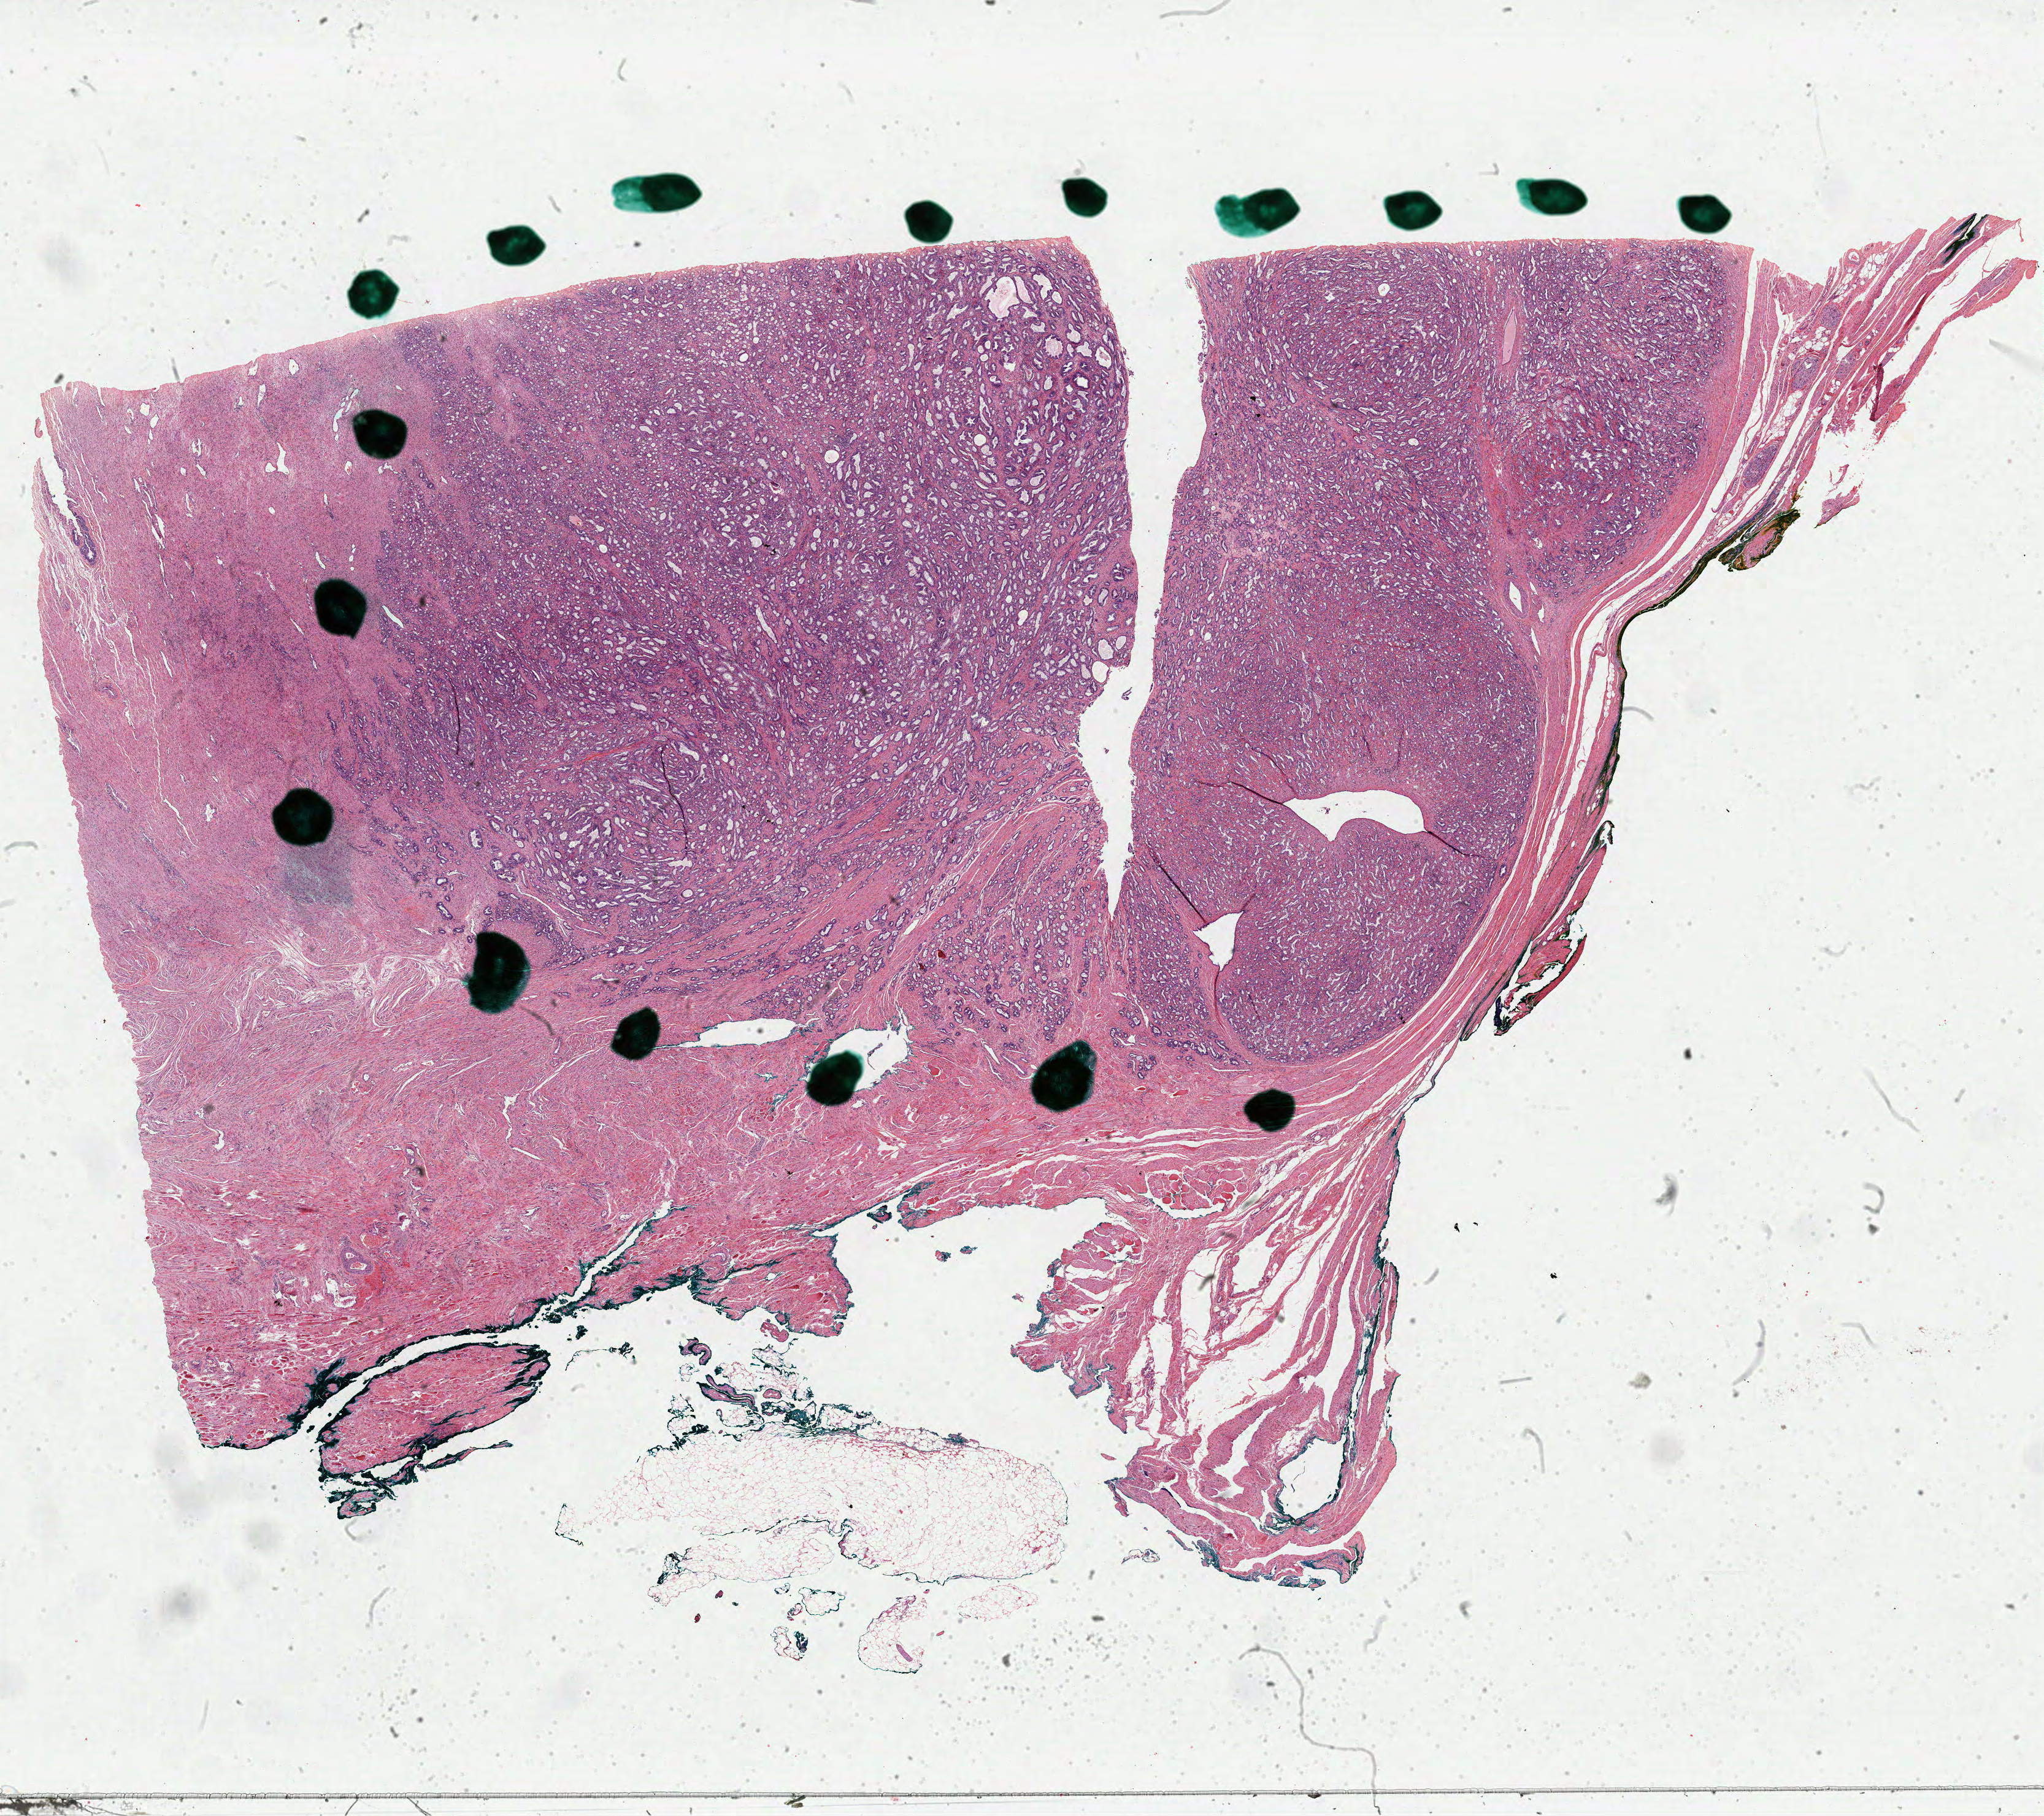
H&E whole-slide image — shown as a low-resolution overview of the whole scanned area (about 26.3 x 23.4 mm, from a 40x scan); formalin-fixed paraffin-embedded (FFPE) diagnostic section; primary tumour sample from the prostate. Patient: male, age at initial diagnosis 69 years. Gleason score: 7 (3+4).
Lymph nodes positive (case pathology): 0 of 4 examined. Pathologic diagnosis: Adenocarcinoma, NOS (prostate gland).